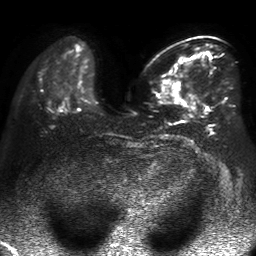
Breast MRI, one axial slice. Diffusion-weighted series; image 2 of 4 stored at this slice position (different b-values; order by instance number). 1.5 T. 256 × 256 image matrix. Female patient.
Outlined on this slice (manually delineated by an expert):
- tumour on diffusion-weighted imaging: bounding box [x1, y1, x2, y2] px = [171, 57, 185, 90]